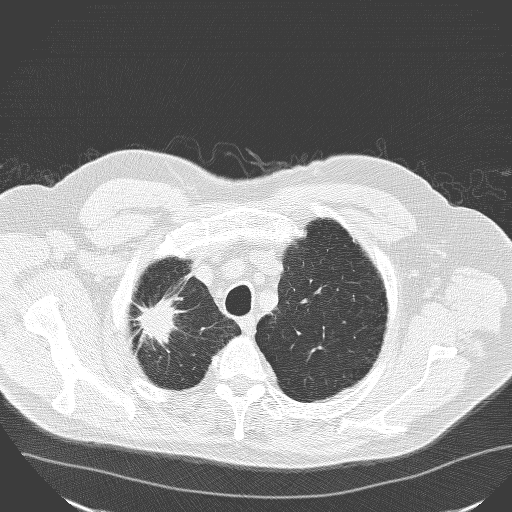
Chest CT (low-dose screening protocol), one axial image; baseline screening round; lung window (W 1500 / L -600 HU); lung (sharp) reconstruction kernel (D); 120 kVp; 512 × 512 image matrix, field of view 400 × 400 mm. Male, age 71 years at enrolment.
Expert-annotated lung lesion, bounding box [x1, y1, x2, y2] px = [117, 285, 189, 359]. Screening reader's record for this exam (one nodule recorded; not confirmed to be the boxed lesion): non-calcified nodule or mass ≥4 mm, right upper lobe, 30 × 25 mm, spiculated (stellate) margins, soft tissue attenuation. Official screen result: positive, change unspecified: nodule(s) >= 4 mm or enlarging nodule(s), mass(es), or other non-specific abnormalities suspicious for lung cancer. Participant outcome: lung cancer diagnosed 182 days after this screen — squamous cell carcinoma, NOS, right upper lobe, poorly differentiated (G3), stage IA (AJCC 6th edition), 30 mm at pathology.